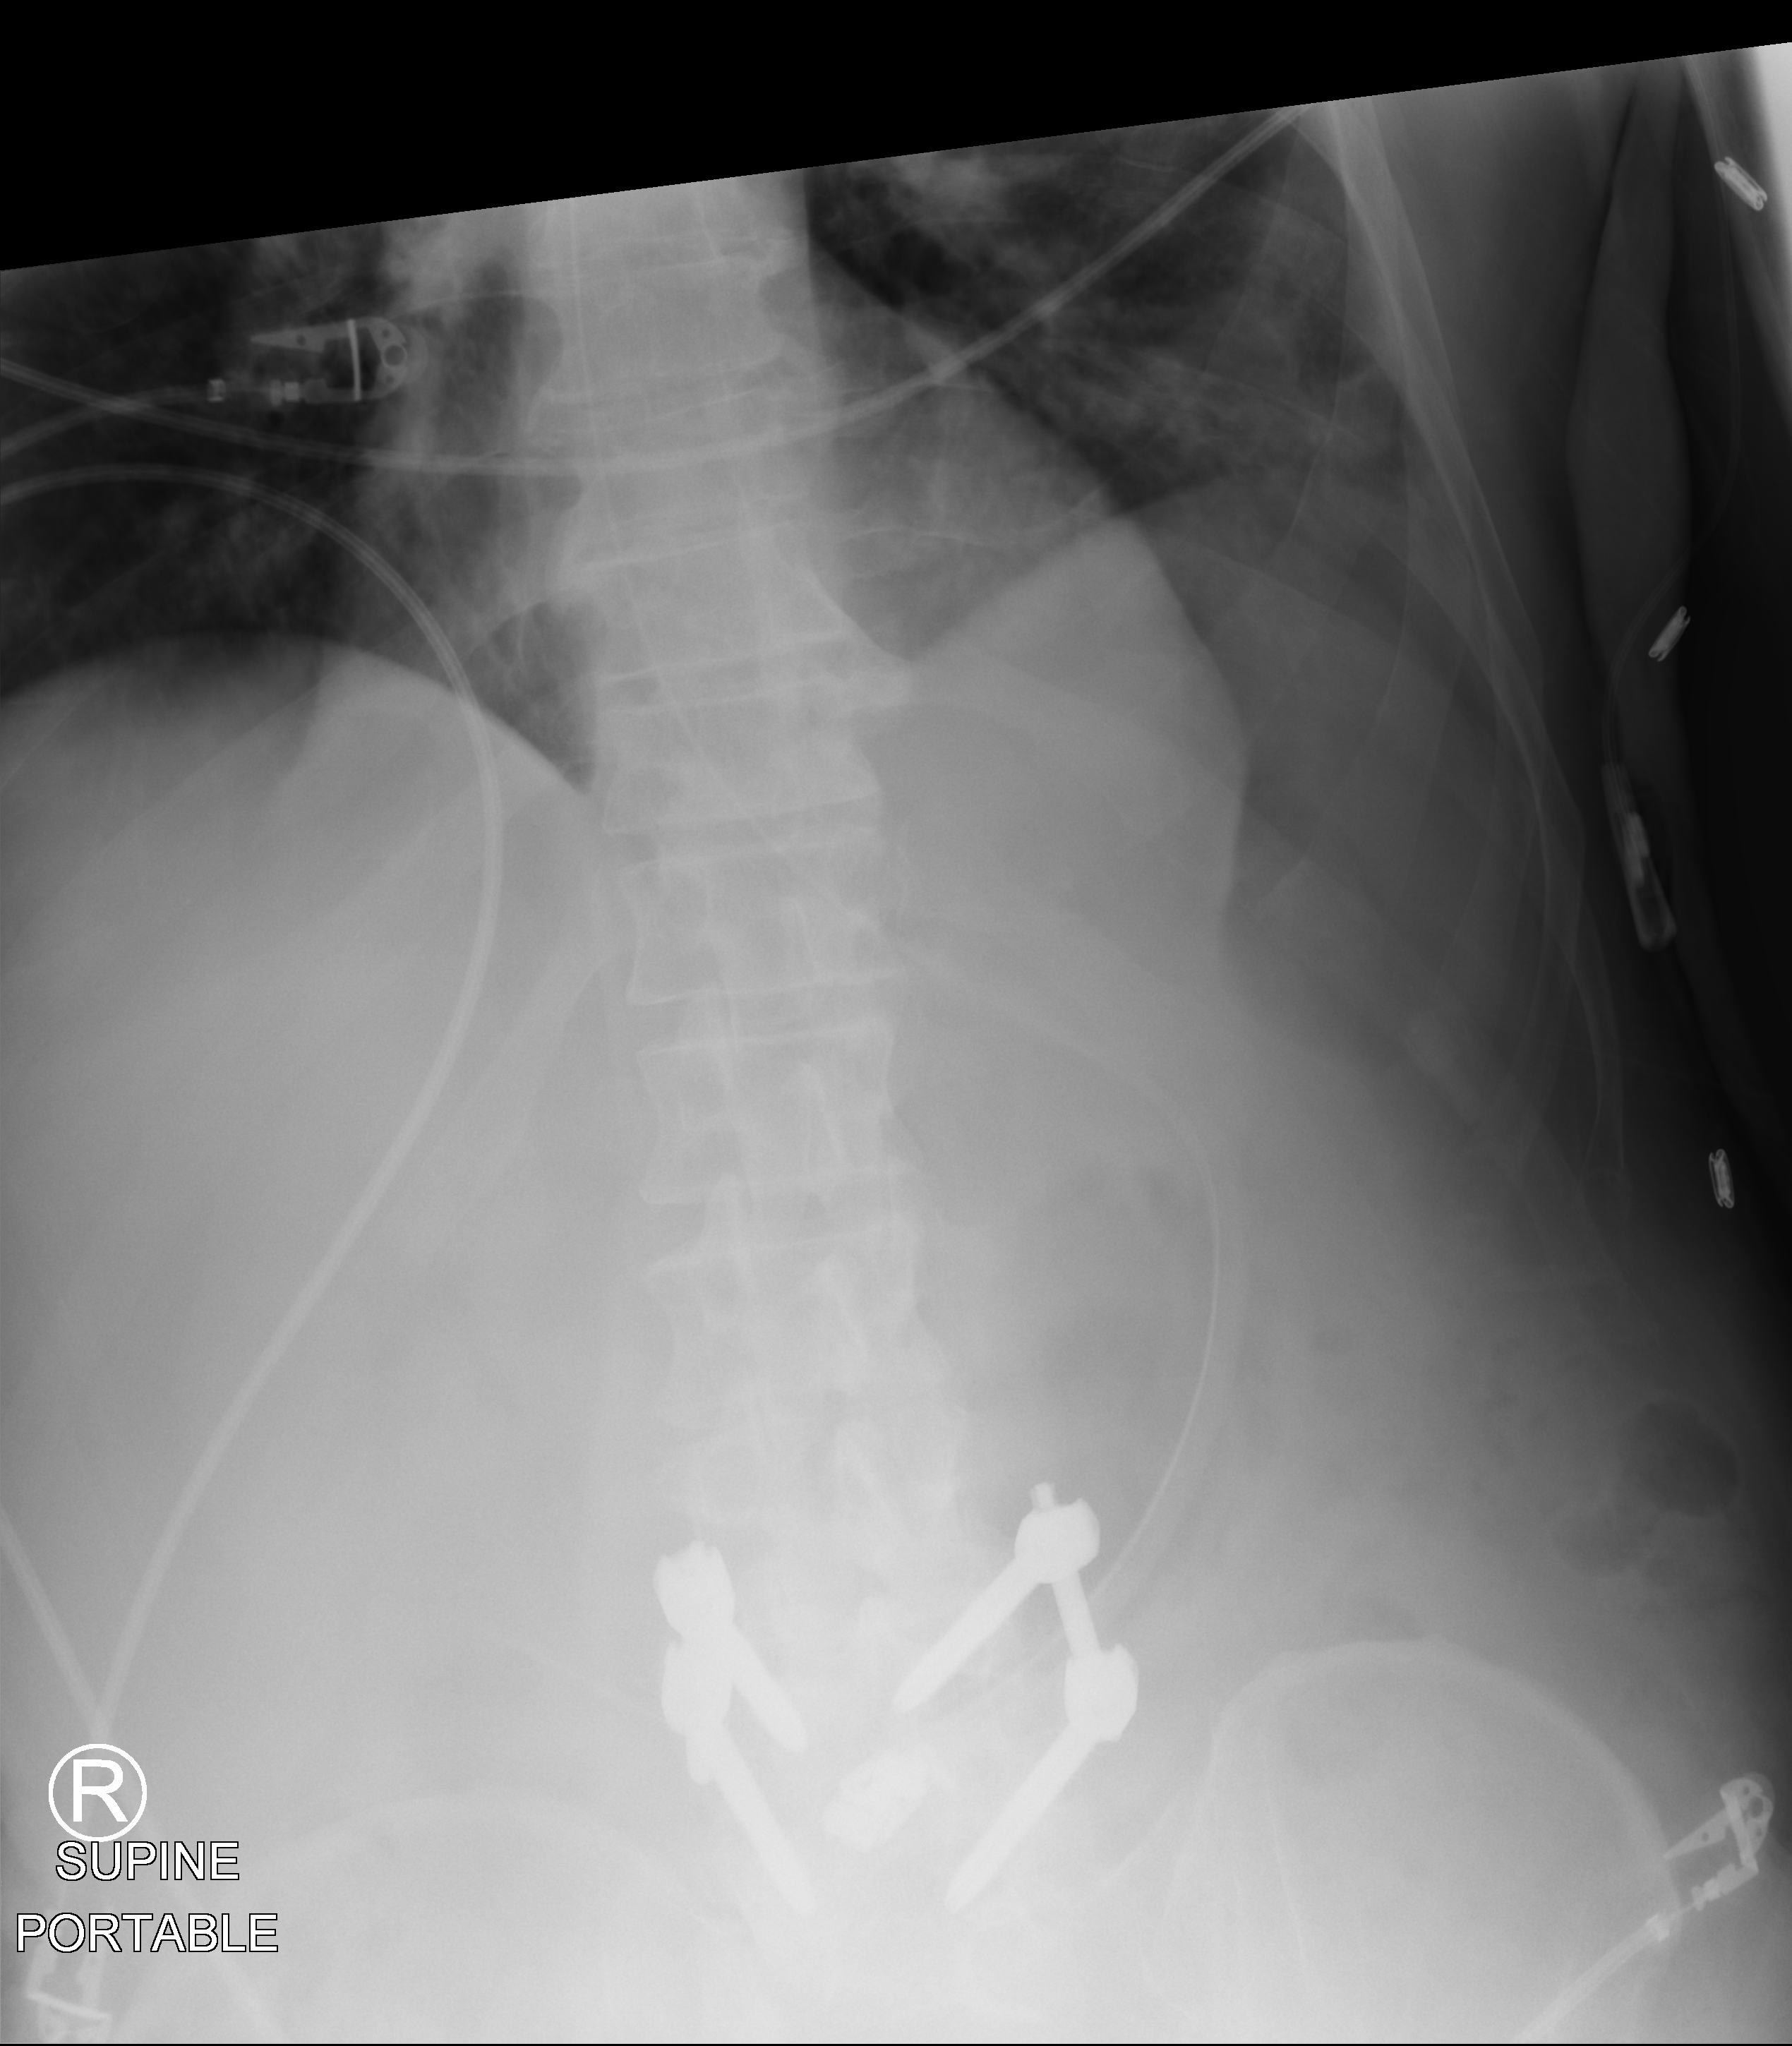
Bedside abdomen radiograph (computed radiography); anteroposterior (AP) projection. Male patient hospitalised with COVID-19, age 60–74 years.
From the hospital-stay record, not from the radiograph (when in the stay this image was taken is not recorded):
- other chronic lung disease (admission record): no
- chronic kidney disease (admission record): no
- admitted to intensive care during this hospital stay: yes